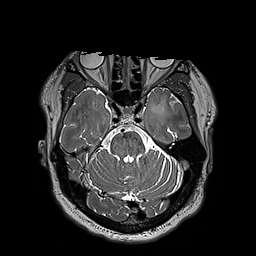
Brain MRI from a brain-tumour surgery series, one axial slice; position 131 of 192 along the scan axis; 1 mm slice thickness; 256 × 256 image matrix. From the clinical record (not read from this slice): histopathology: Astrocytoma; WHO grade: 3; IDH mutation: yes.
Annotated regions visible in this slice (expert manual segmentation):
- tumour: box from (x=150, y=98) to (x=166, y=118) px